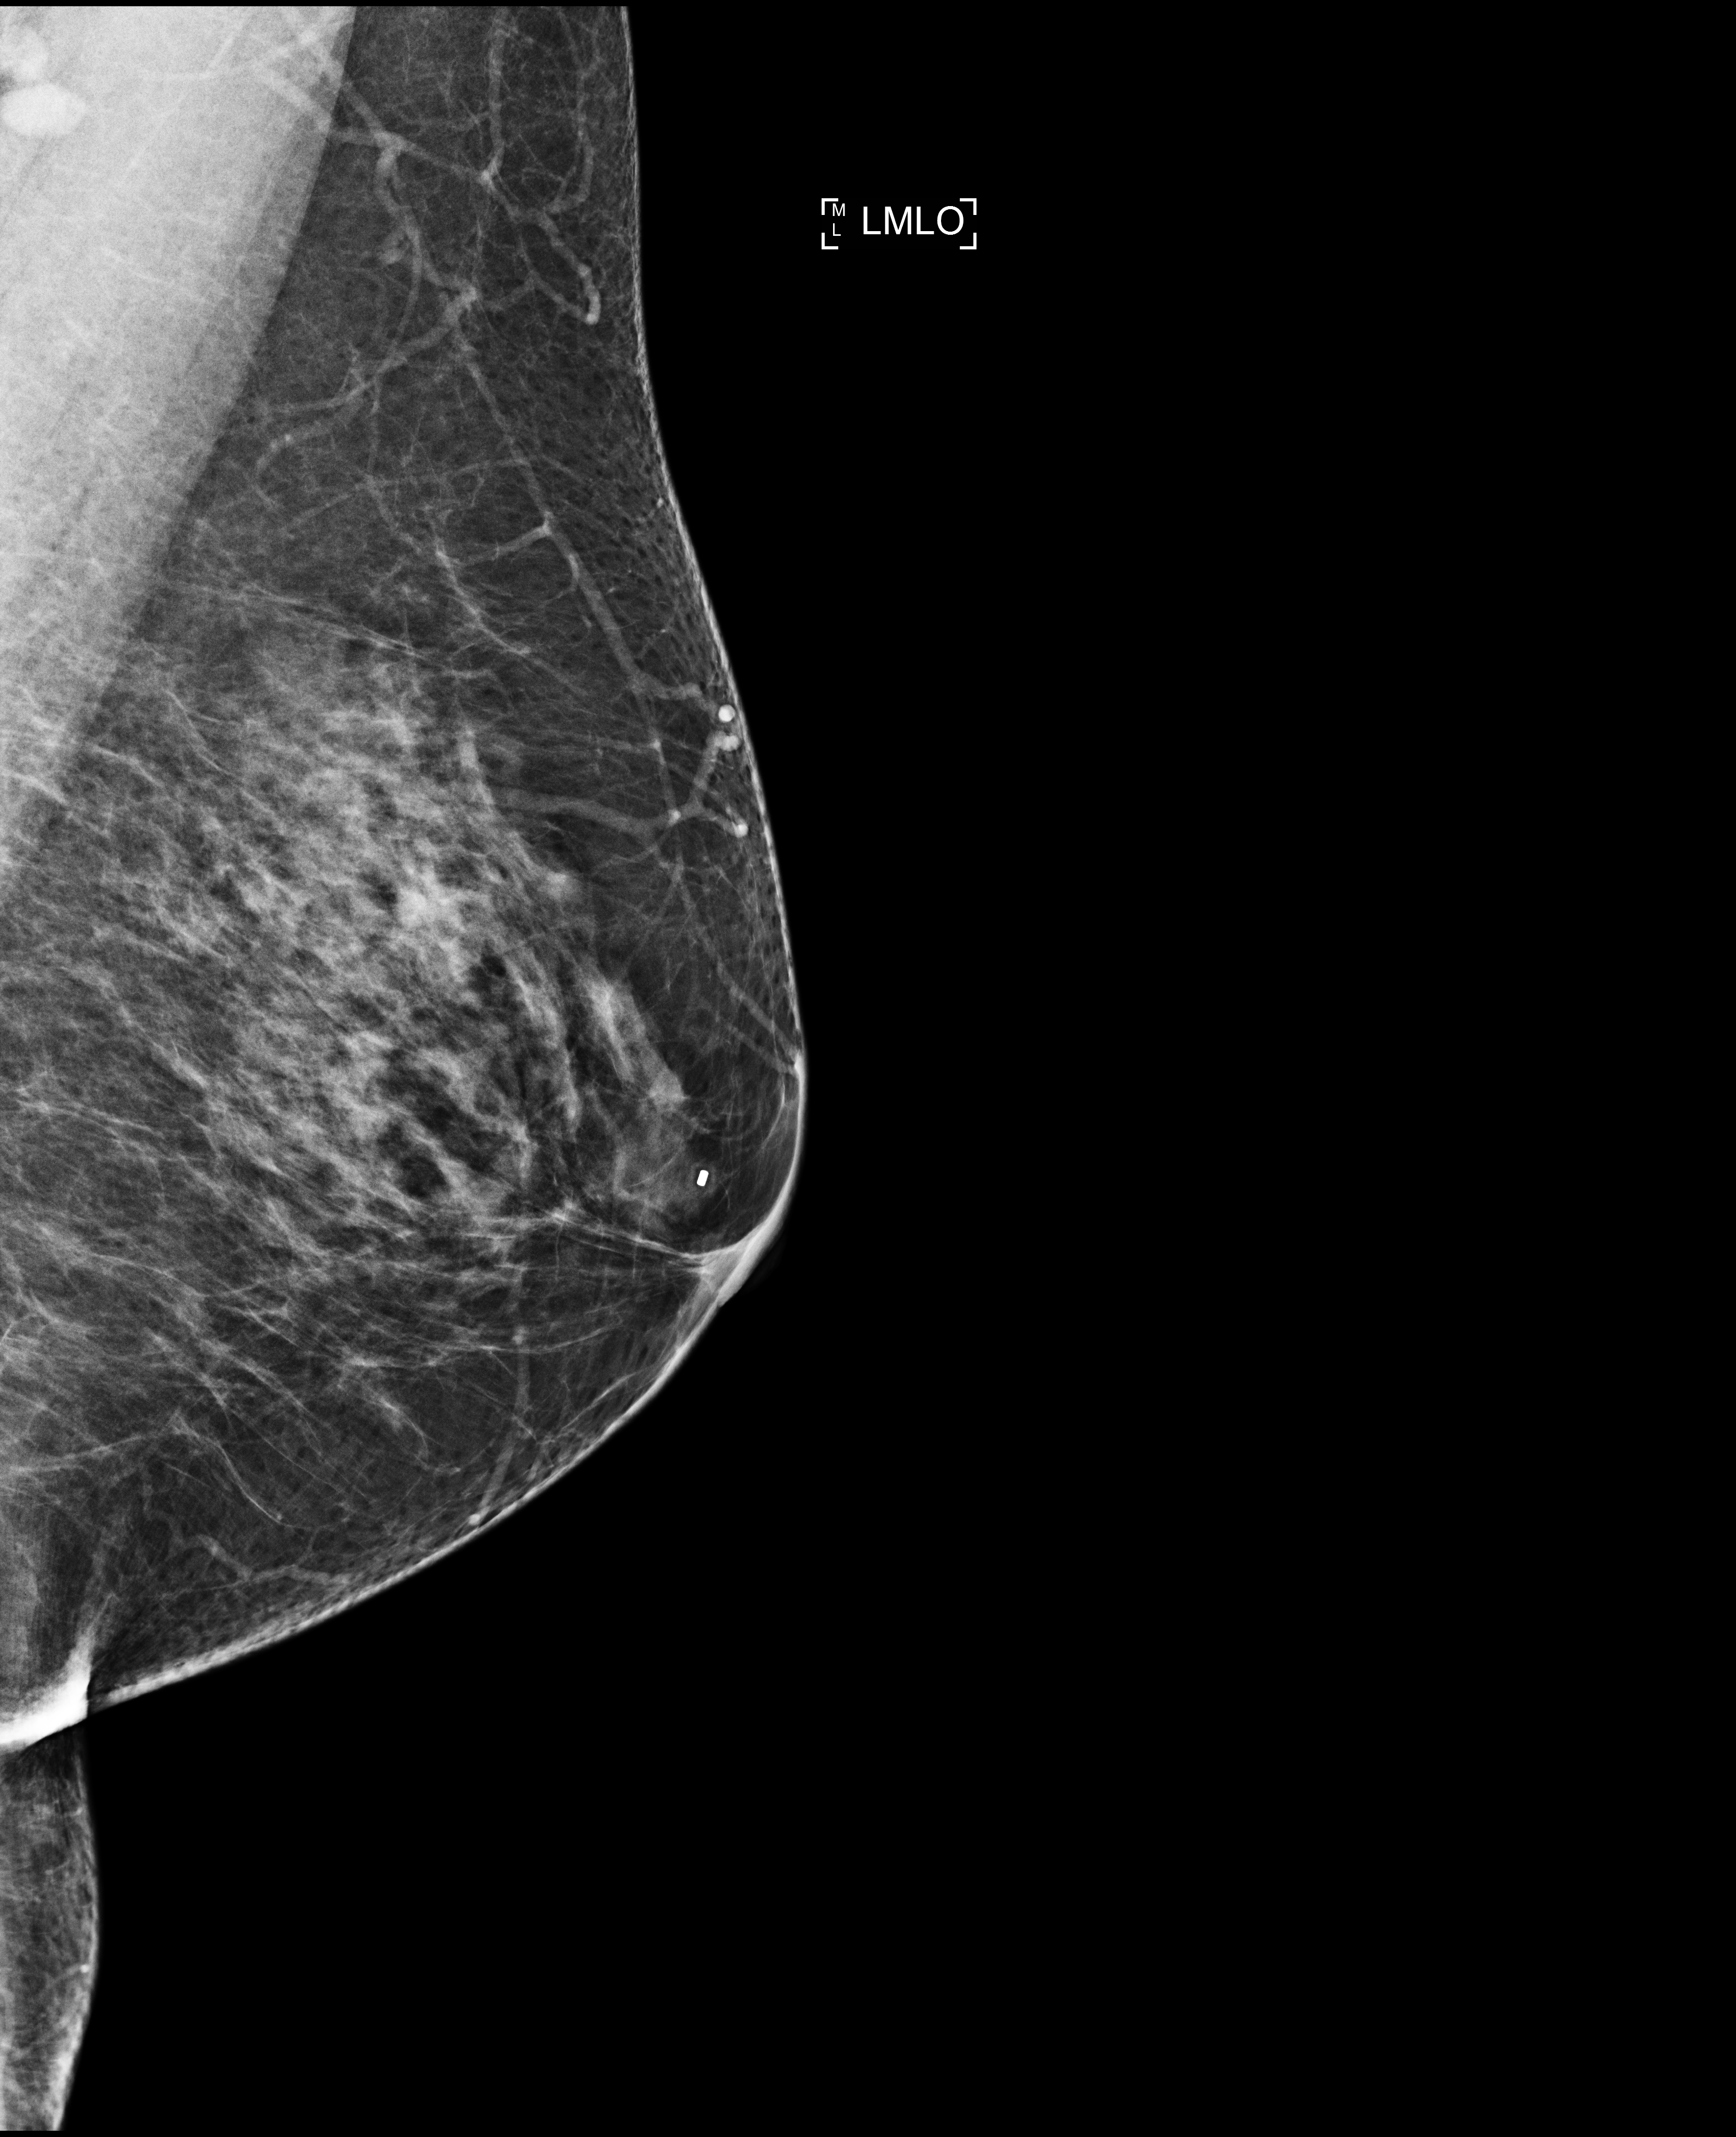
Screening examination, compressed breast thickness 62 mm. Patient aged 56 years (female).
Image type: full-field digital mammogram. Breast: left. Projection: mediolateral oblique (MLO) view.